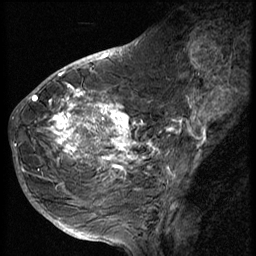
Breast MRI (dynamic contrast-enhanced), one sagittal slice; position 24 of 56 along the scan axis; 3 images stored at this slice position (order not interpretable as contrast timing); 1.5 T; TE 4.2 ms, TR 9 ms; 2.5 mm slice thickness; 256 × 256 image matrix, field of view 180 × 180 mm. Patient: female, 49 years. From the clinical record (not read from this slice): setting: breast cancer imaged before/during neoadjuvant chemotherapy; receptor status: HER2-positive.
Structures marked on this image (semi-automatically segmented with operator editing):
- analysis volume of interest (the breast-tissue region the enhancement analysis was run in; not a lesion): box from (x=37, y=85) to (x=141, y=207) px
- tumour enhancement mask (voxels above the 140 % enhancement threshold inside the analysis volume of interest): (x=37, y=85)–(x=140, y=179)